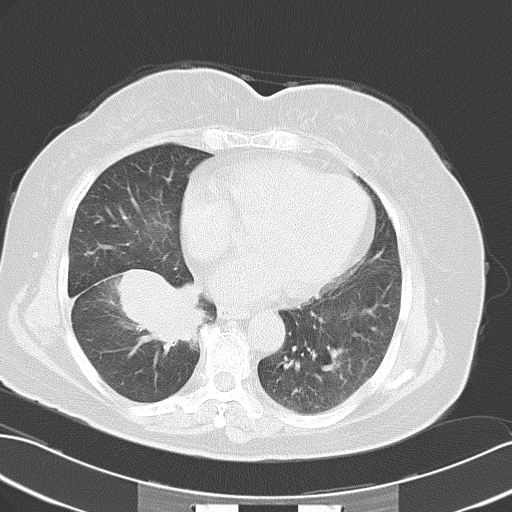
Chest CT, one axial slice. Position 21 of 50 along the scan axis. 120 kVp. Lung window (W 1500 / L -600 HU). 512 × 512 image matrix, field of view 353 × 353 mm. Female patient, age 63 years. From the clinical record (not read from this slice): clinical TNM (as recorded): T3 N0 M0.
Outlined on this slice (rectangle marked by the reading radiologist):
- lung tumour (recorded histology: adenocarcinoma): bounding box (x1, y1, x2, y2) in pixels: (115, 261, 204, 350)